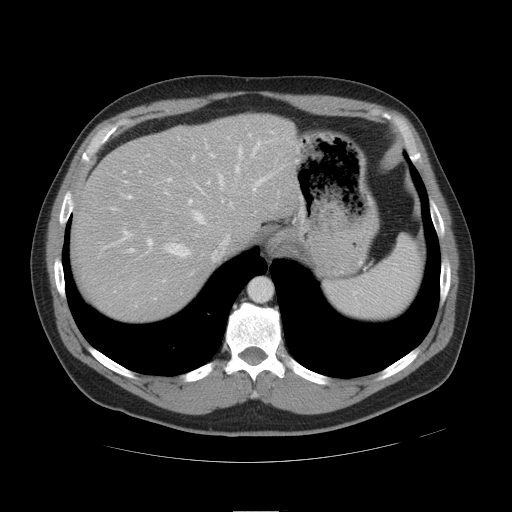
Contrast-enhanced abdominal CT, one axial slice. Position 37 of 49 along the scan axis. Soft-tissue window (W 400 / L 40 HU). 5 mm slice thickness. 512 × 512 image matrix, field of view 425 × 425 mm. Male patient, age 52 years. Case-level facts recorded for this patient, not image findings: diagnosis: colorectal cancer liver metastases, imaged before liver resection; multiple liver metastases: yes; largest metastasis: 5.1 cm; disease in both lobes: yes.
Structures marked on this image (manually delineated by an expert):
- hepatic veins: bounding box <128,140,262,299> (left, top, right, bottom; pixels)
- liver: <72,118,294,318>
- planned liver remnant (the part of the liver to remain after resection): <128,118,295,243>
- portal vein (with intrahepatic branches): <119,133,272,250>